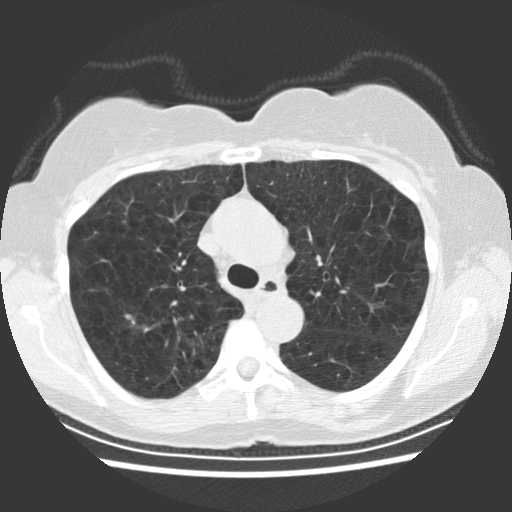
Axial slice from a low-dose chest CT screening exam, baseline annual screen, lung window (W 1500 / L -600 HU), standard (soft-tissue) reconstruction kernel (STANDARD), slice 67 of 234 in the series, 512 × 512 image matrix. Female participant, aged 66 years at enrolment.
Expert reader's lesion annotation, bounding box [x1, y1, x2, y2] px = [112, 297, 154, 339]. Screening reader's record for this exam (one nodule recorded; not confirmed to be the boxed lesion): non-calcified nodule or mass ≥4 mm, right upper lobe, 10 × 8 mm, smooth margins, soft tissue attenuation. Later outcome: lung cancer diagnosed 54 days after this screen — squamous cell carcinoma, keratinizing, NOS, right upper lobe, poorly differentiated (G3), stage IA (AJCC 6th edition), 11 mm at pathology.